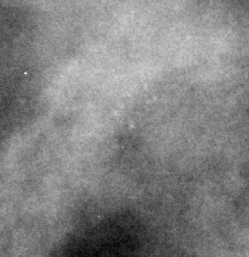
Region of interest cut from a scanned film mammogram (one marked finding), right breast, MLO view.
- Finding: calcifications, morphology pleomorphic, distribution clustered; BI-RADS assessment category 4; subtlety rating 2 on a 1 (subtle) to 5 (obvious) scale; pathology result (as recorded, not read from the image): benign.